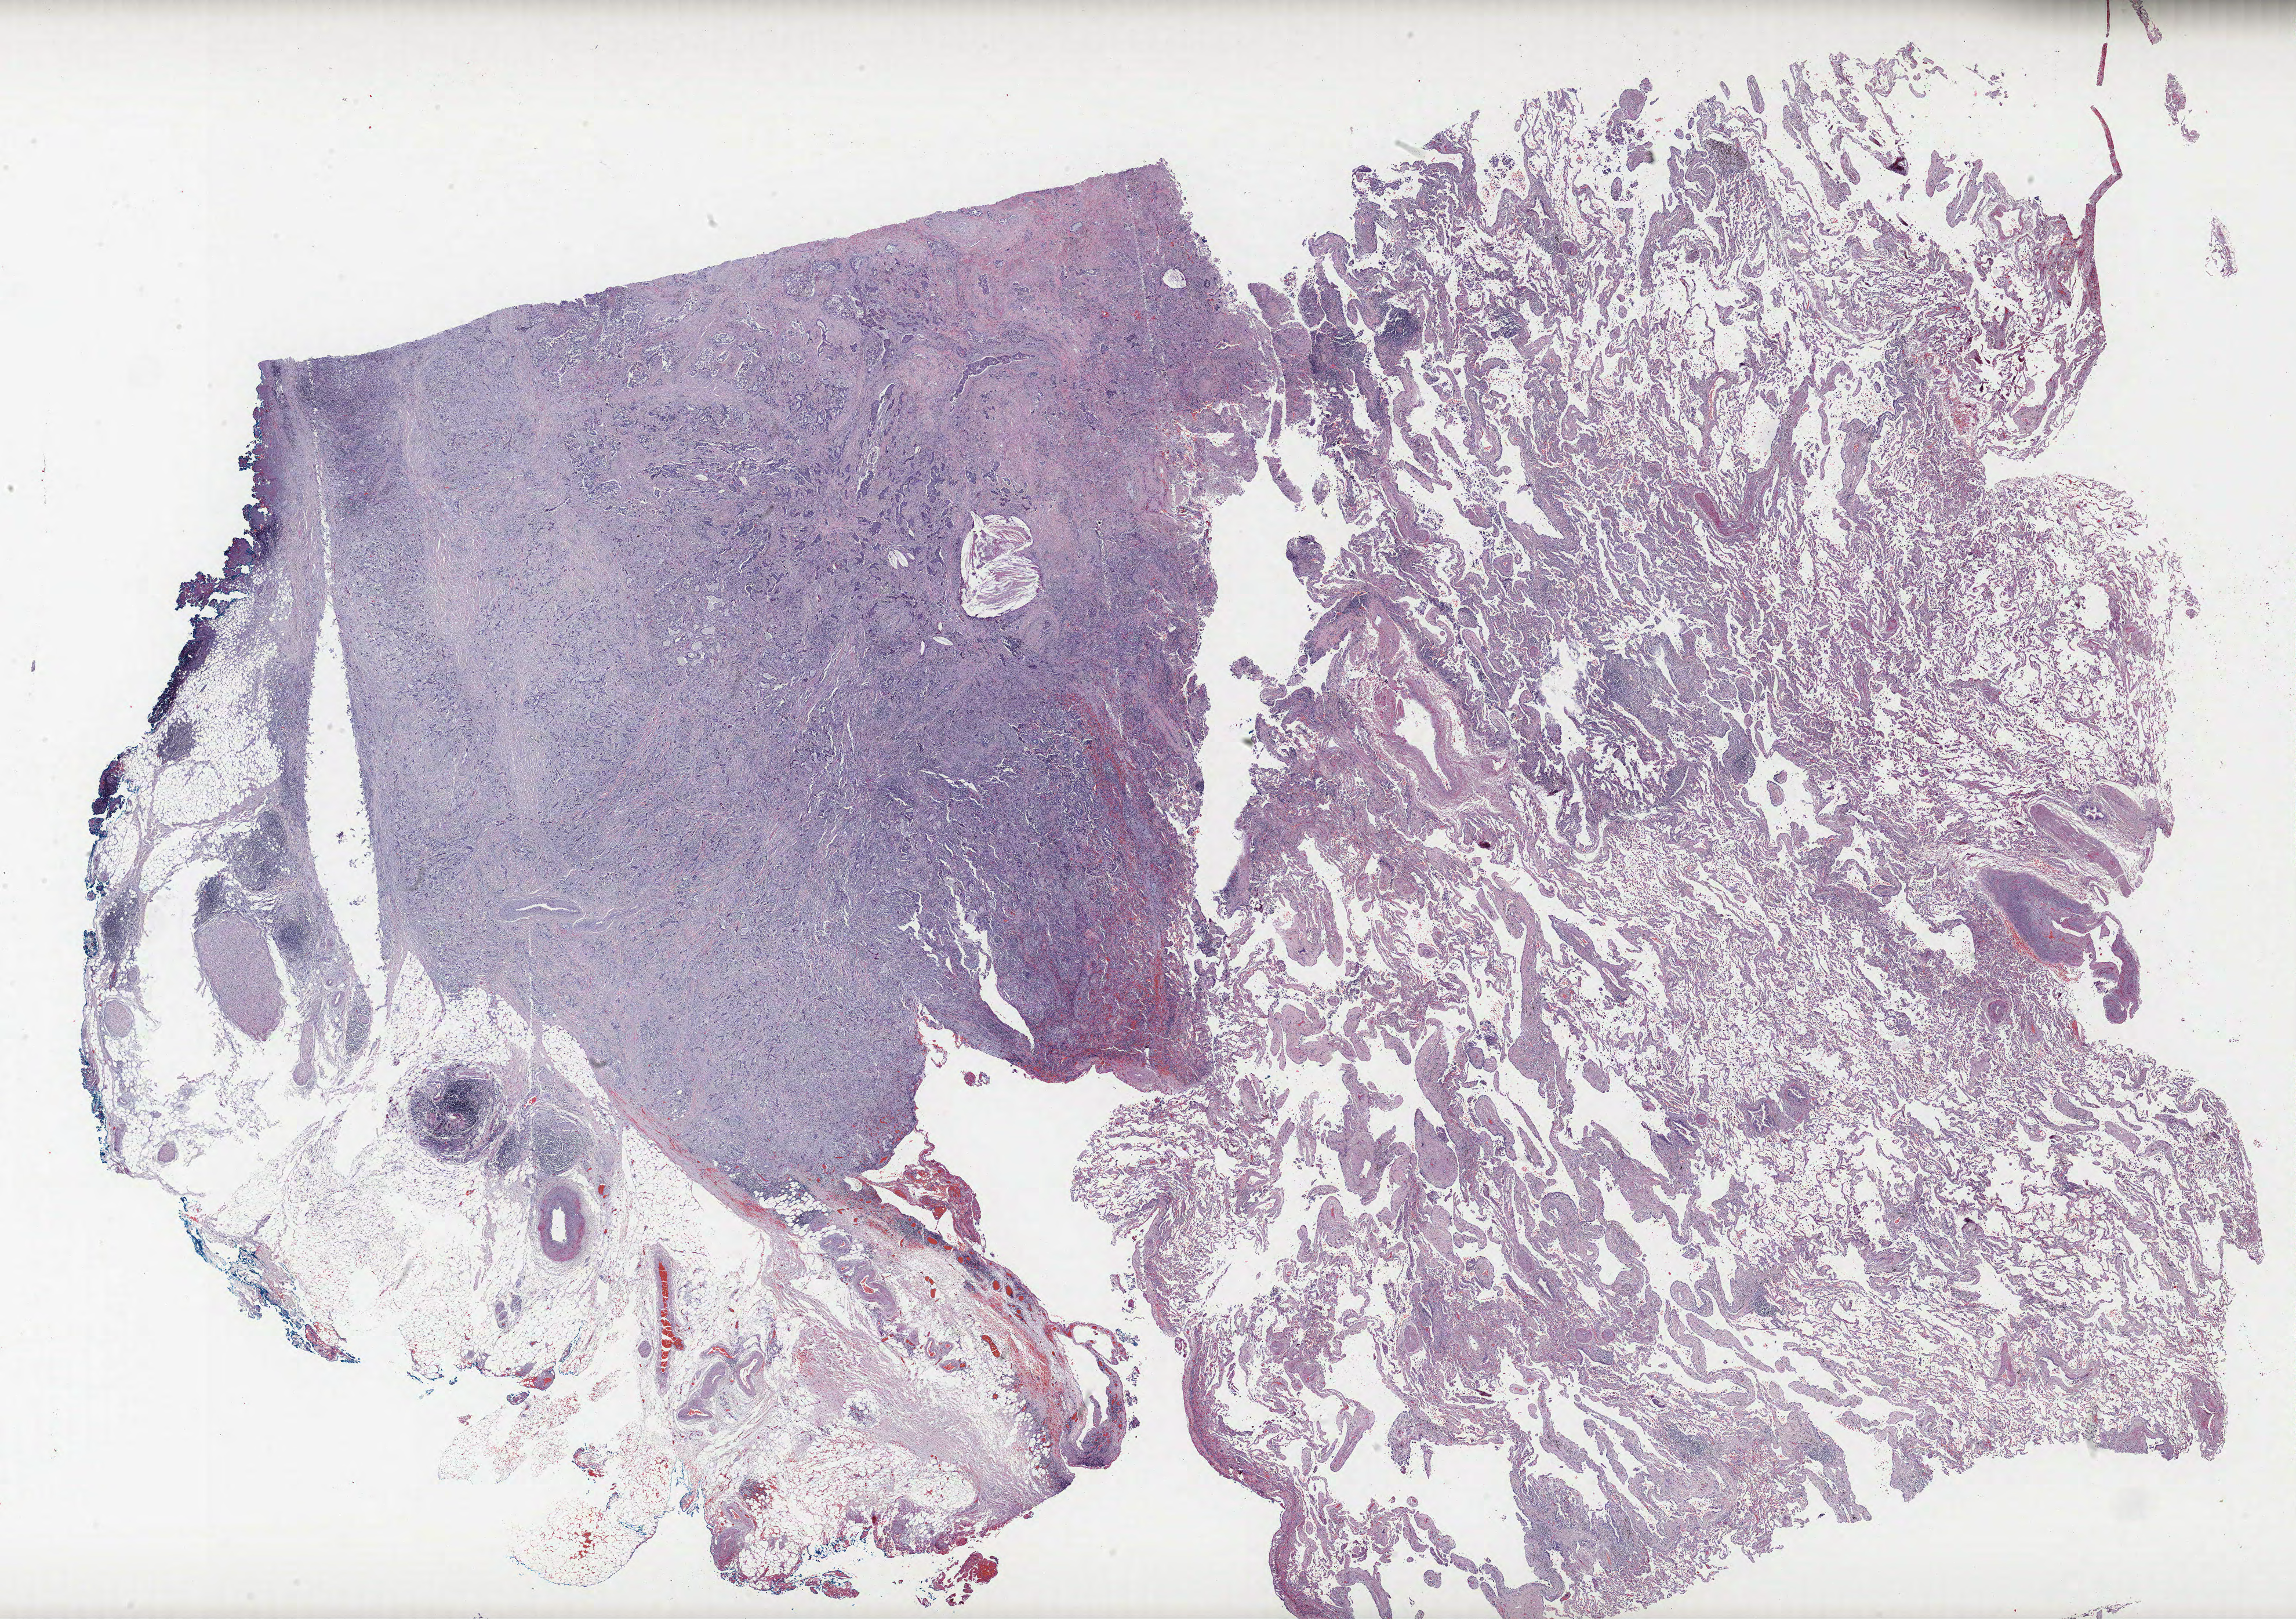
H&E-stained whole-slide image — shown as a low-resolution overview of the whole scanned area (about 31.7 x 22.3 mm, acquisition: 40x scan), FFPE section, lung tissue. Female patient, aged 56 at enrolment. Grade: well differentiated (G1).
Primary tumour location (clinical record): left upper lobe. Participant's lung-cancer diagnosis: Mucin-producing adenocarcinoma (ICD-O-3 8481/3). Stage (AJCC 6th edition): IIB. Tumour size (pathology): 30 mm.